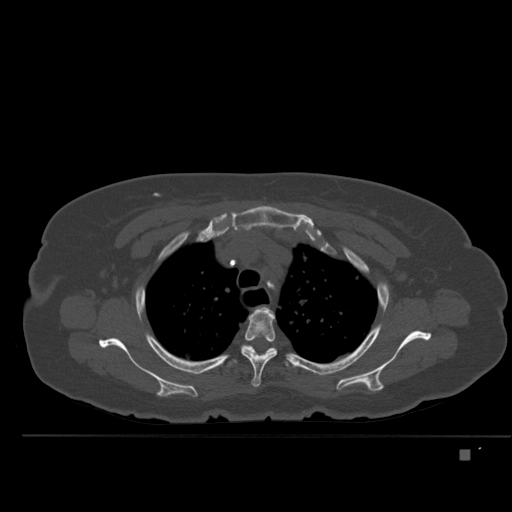
CT including the spine, one axial slice; slice 377 of 477 in the series (ordered by position); bone window (W 1800 / L 400 HU); 1.5 mm slice thickness; 512 × 512 image matrix, field of view 422 × 422 mm. Patient: female, 74 years. From the clinical record (not read from this slice): primary cancer: colon.
Structures marked on this image (semi-automatic segmentation, software-assisted and operator-edited):
- T3 vertebra: box from (x=241, y=307) to (x=277, y=387) px
- T4 vertebra: (x=227, y=345)–(x=298, y=368)